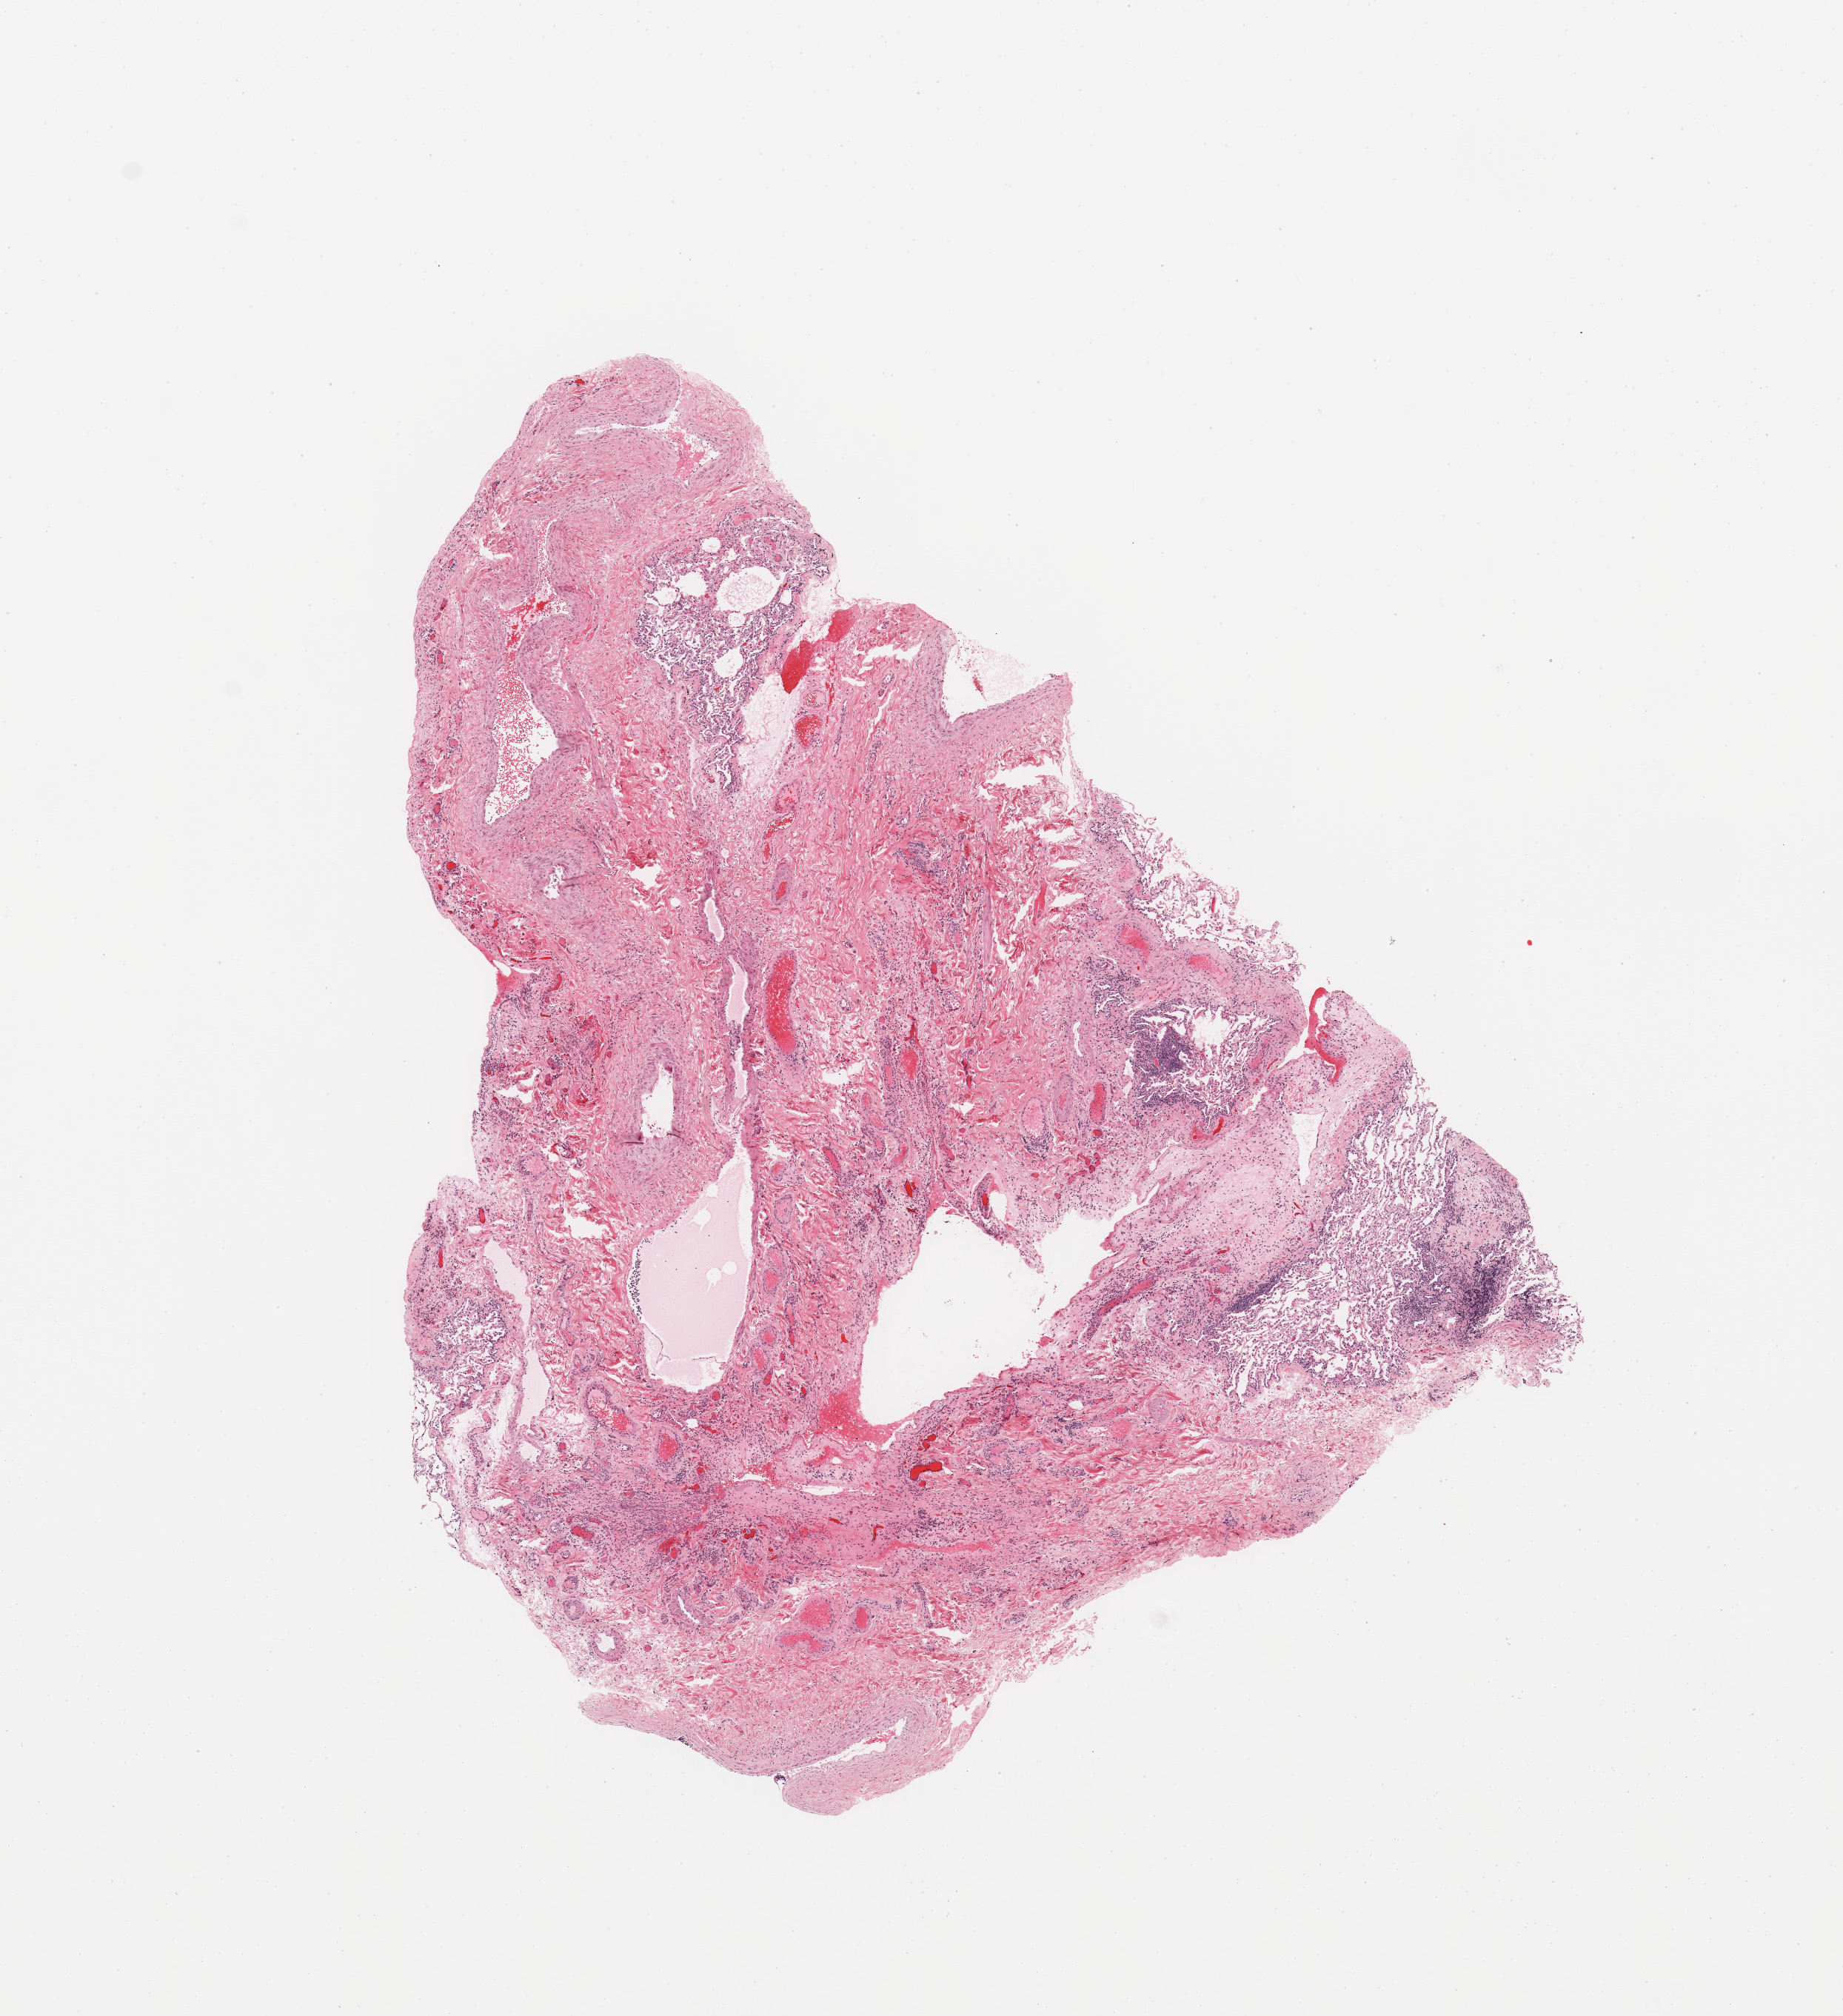
H&E whole-slide image, a low-resolution overview of the entire scanned area, about 9.8 x 10.8 mm; normal (non-tumour) tissue sample, sampled site: lung. Female, 73 y/o.
This section: normal (non-tumour) tissue from the same patient. Patient diagnosis: Adenocarcinoma, NOS.